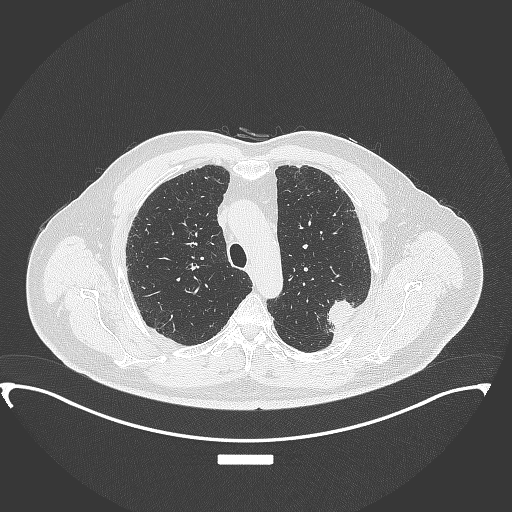
Chest CT, one axial slice; slice 270 of 350 in the series (ordered by position); reconstruction kernel B70f; 120 kVp; lung window (W 1500 / L -600 HU); 1 mm slice thickness; 512 × 512 image matrix, field of view 459 × 459 mm. Patient: male, 64 years. From the clinical record (not read from this slice): clinical TNM (as recorded): T1c N1 M1.
Outlined on this slice (rectangle marked by the reading radiologist):
- lung tumour (recorded histology: adenocarcinoma): box from (x=322, y=294) to (x=359, y=336) px